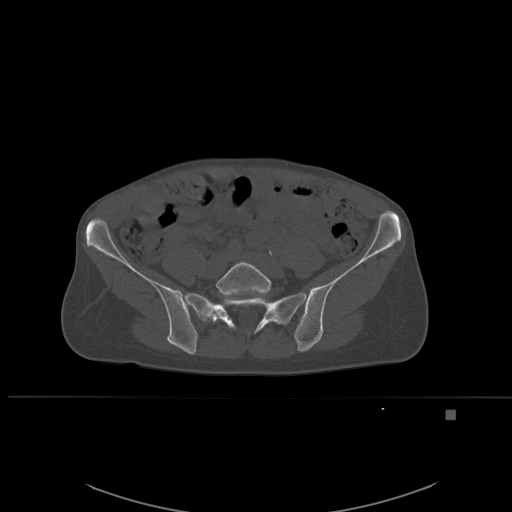
CT including the spine, one axial slice. Position 164 of 537 along the scan axis. Bone window (W 1800 / L 400 HU). 512 × 512 image matrix, field of view 440 × 440 mm. Patient: female, 45 years. From the clinical record (not read from this slice): primary cancer: lung.
Annotated regions visible in this slice (semi-automatic segmentation, software-assisted and operator-edited):
- L5 vertebra: bounding box [x1, y1, x2, y2] px = [216, 261, 271, 299]